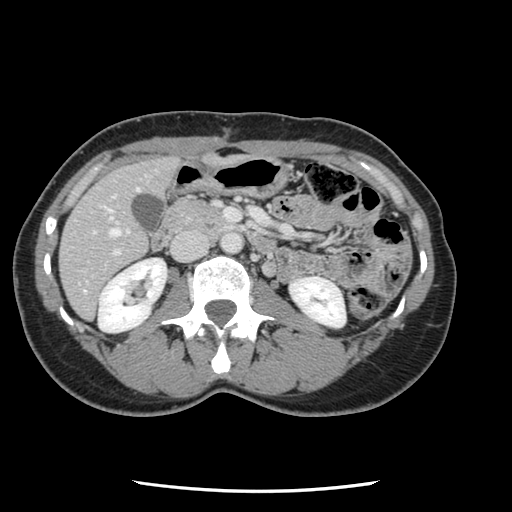
Contrast-enhanced abdominal CT, one axial slice. Position 39 of 134 along the scan axis. 120 kVp. Intravenous contrast given. Soft-tissue window (W 400 / L 40 HU). 2.5 mm slice thickness. 512 × 512 image matrix, field of view 330 × 330 mm. Female patient, age 43 years. From the clinical record (not read from this slice): diagnosis: colorectal cancer liver metastases, imaged before liver resection; multiple liver metastases: yes; largest metastasis: 3.4 cm; chemotherapy before resection: no.
Structures marked on this image (manually delineated by an expert):
- hepatic veins: bounding box (x1, y1, x2, y2) in pixels: (85, 188, 140, 292)
- liver: (60, 158, 179, 318)
- planned liver remnant (the part of the liver to remain after resection): (60, 158, 178, 319)
- portal vein (with intrahepatic branches): (92, 202, 268, 257)